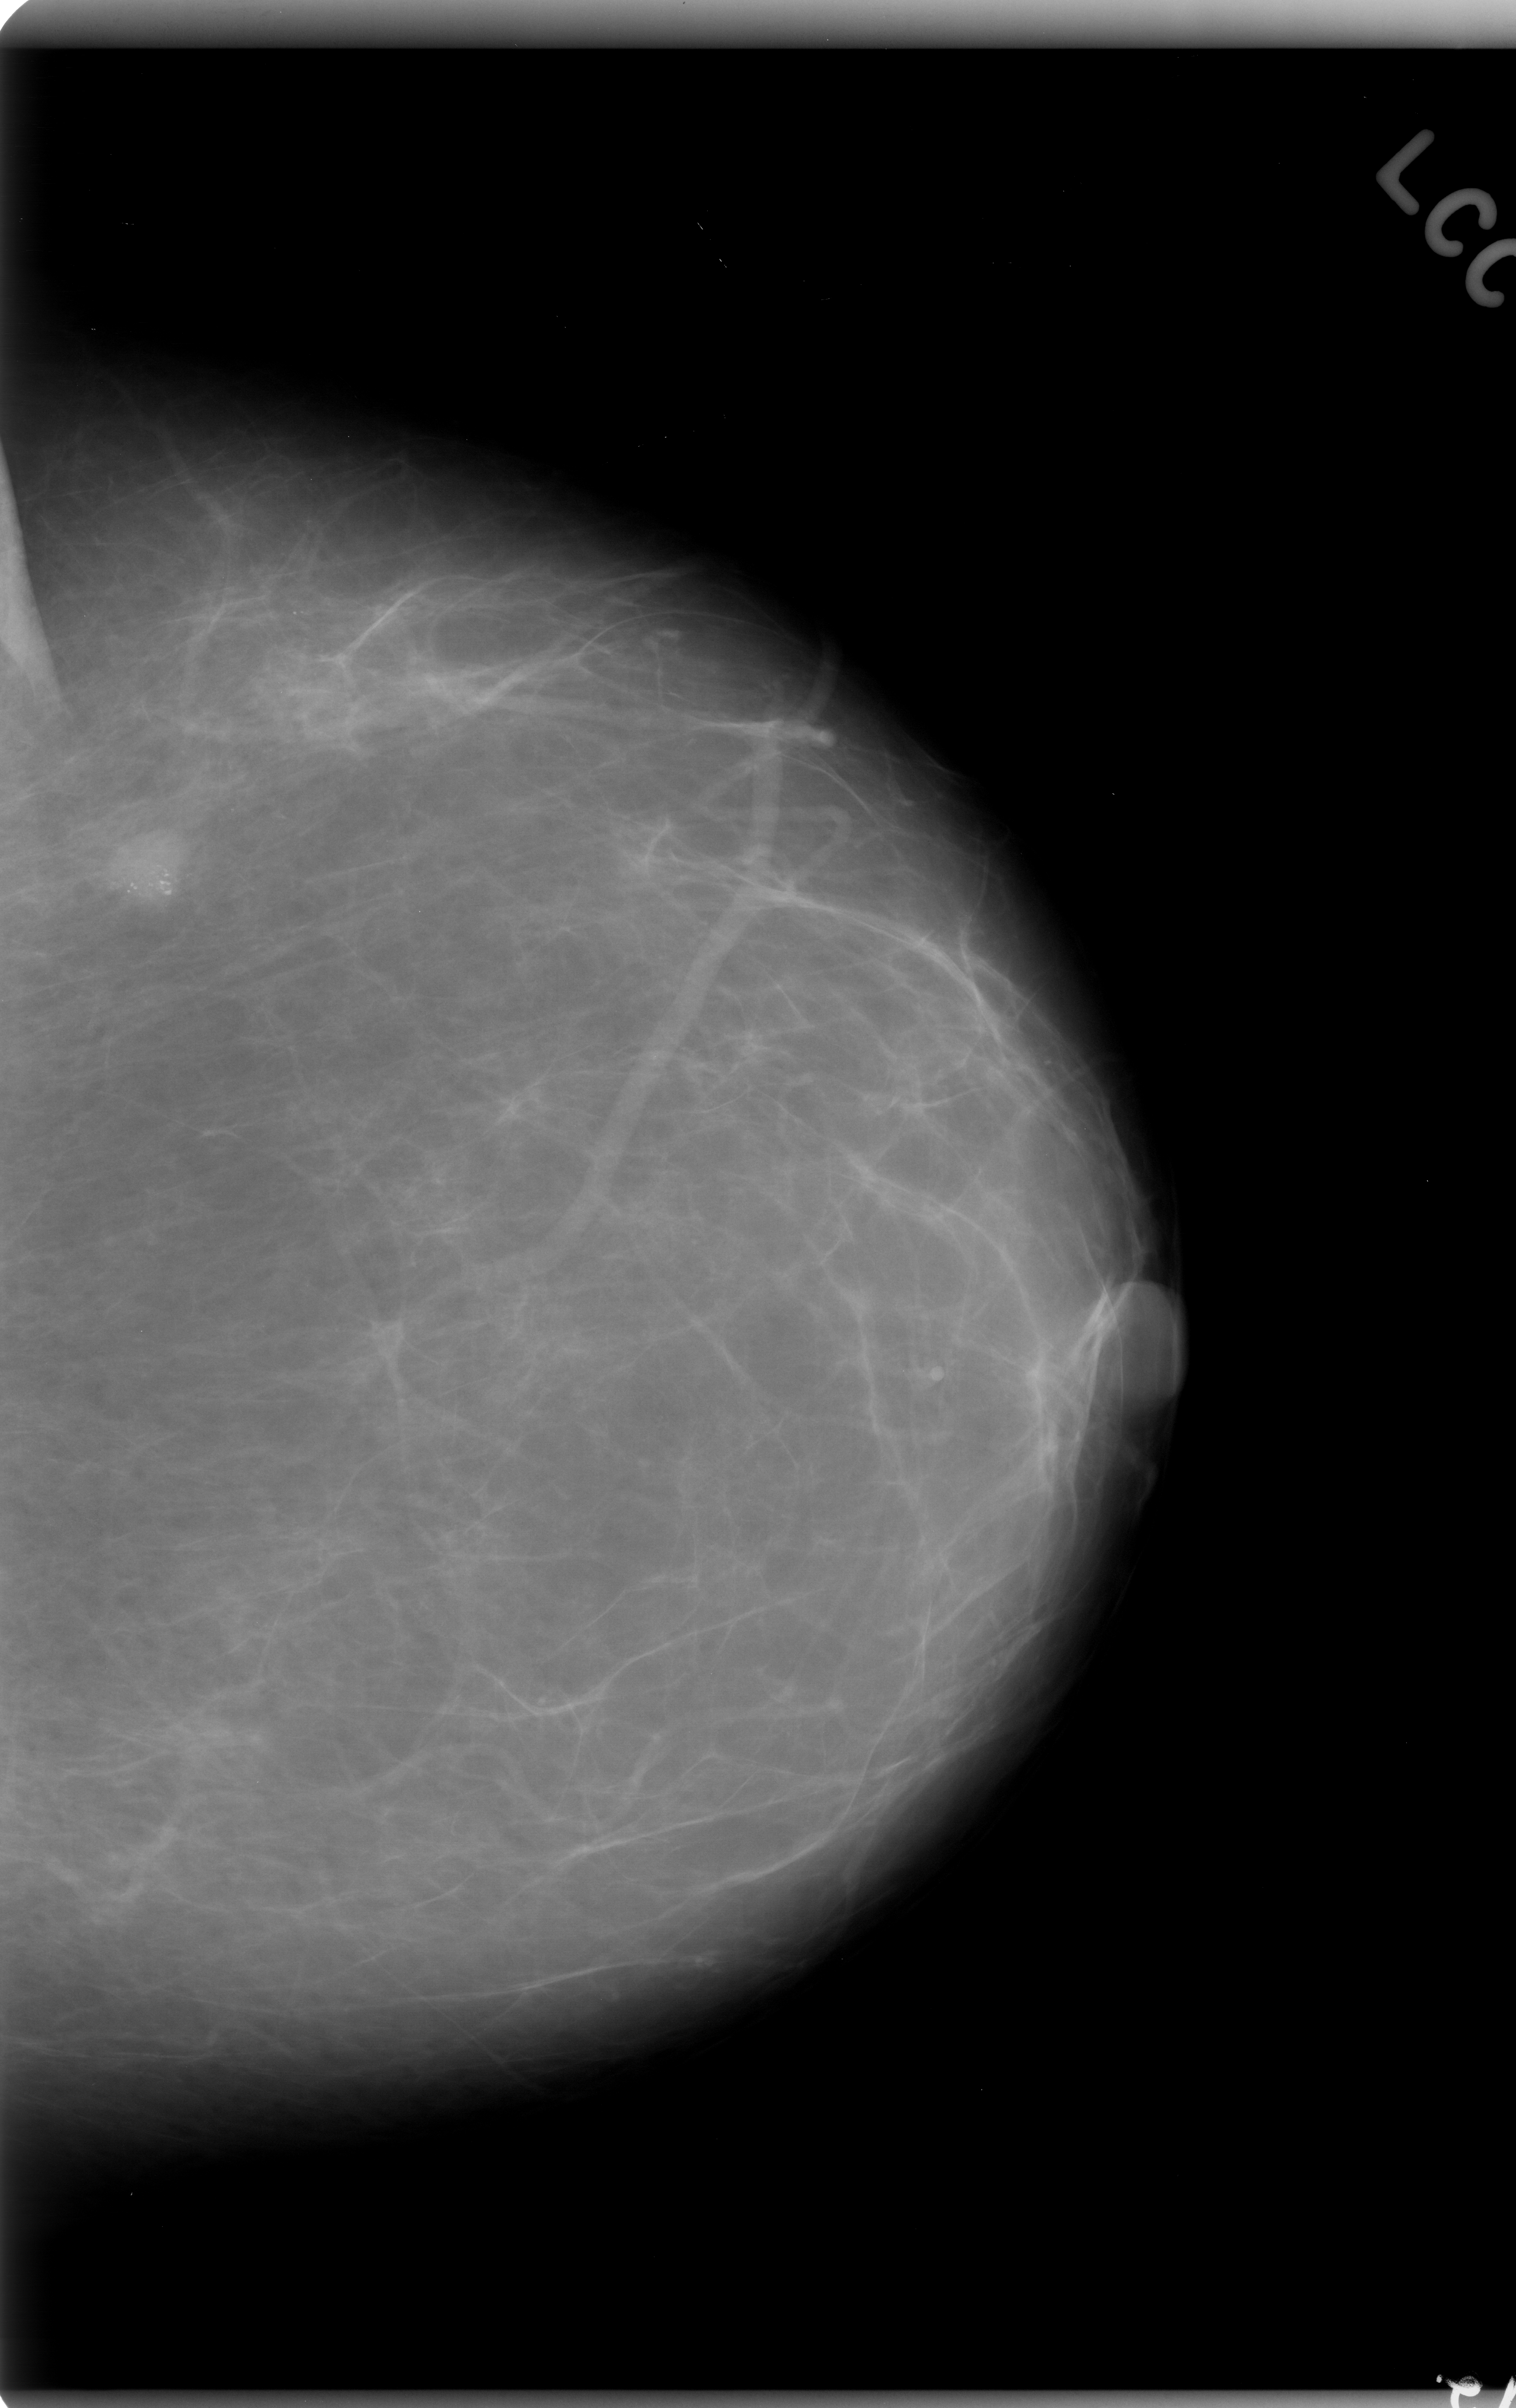
Digitized screen-film mammogram; left breast; CC view; BI-RADS breast density category 1 (scale 1–4).
- Abnormality record for this image: calcifications, morphology pleomorphic, distribution clustered; BI-RADS assessment category 4; pathology result (as recorded, not read from the image): malignant.